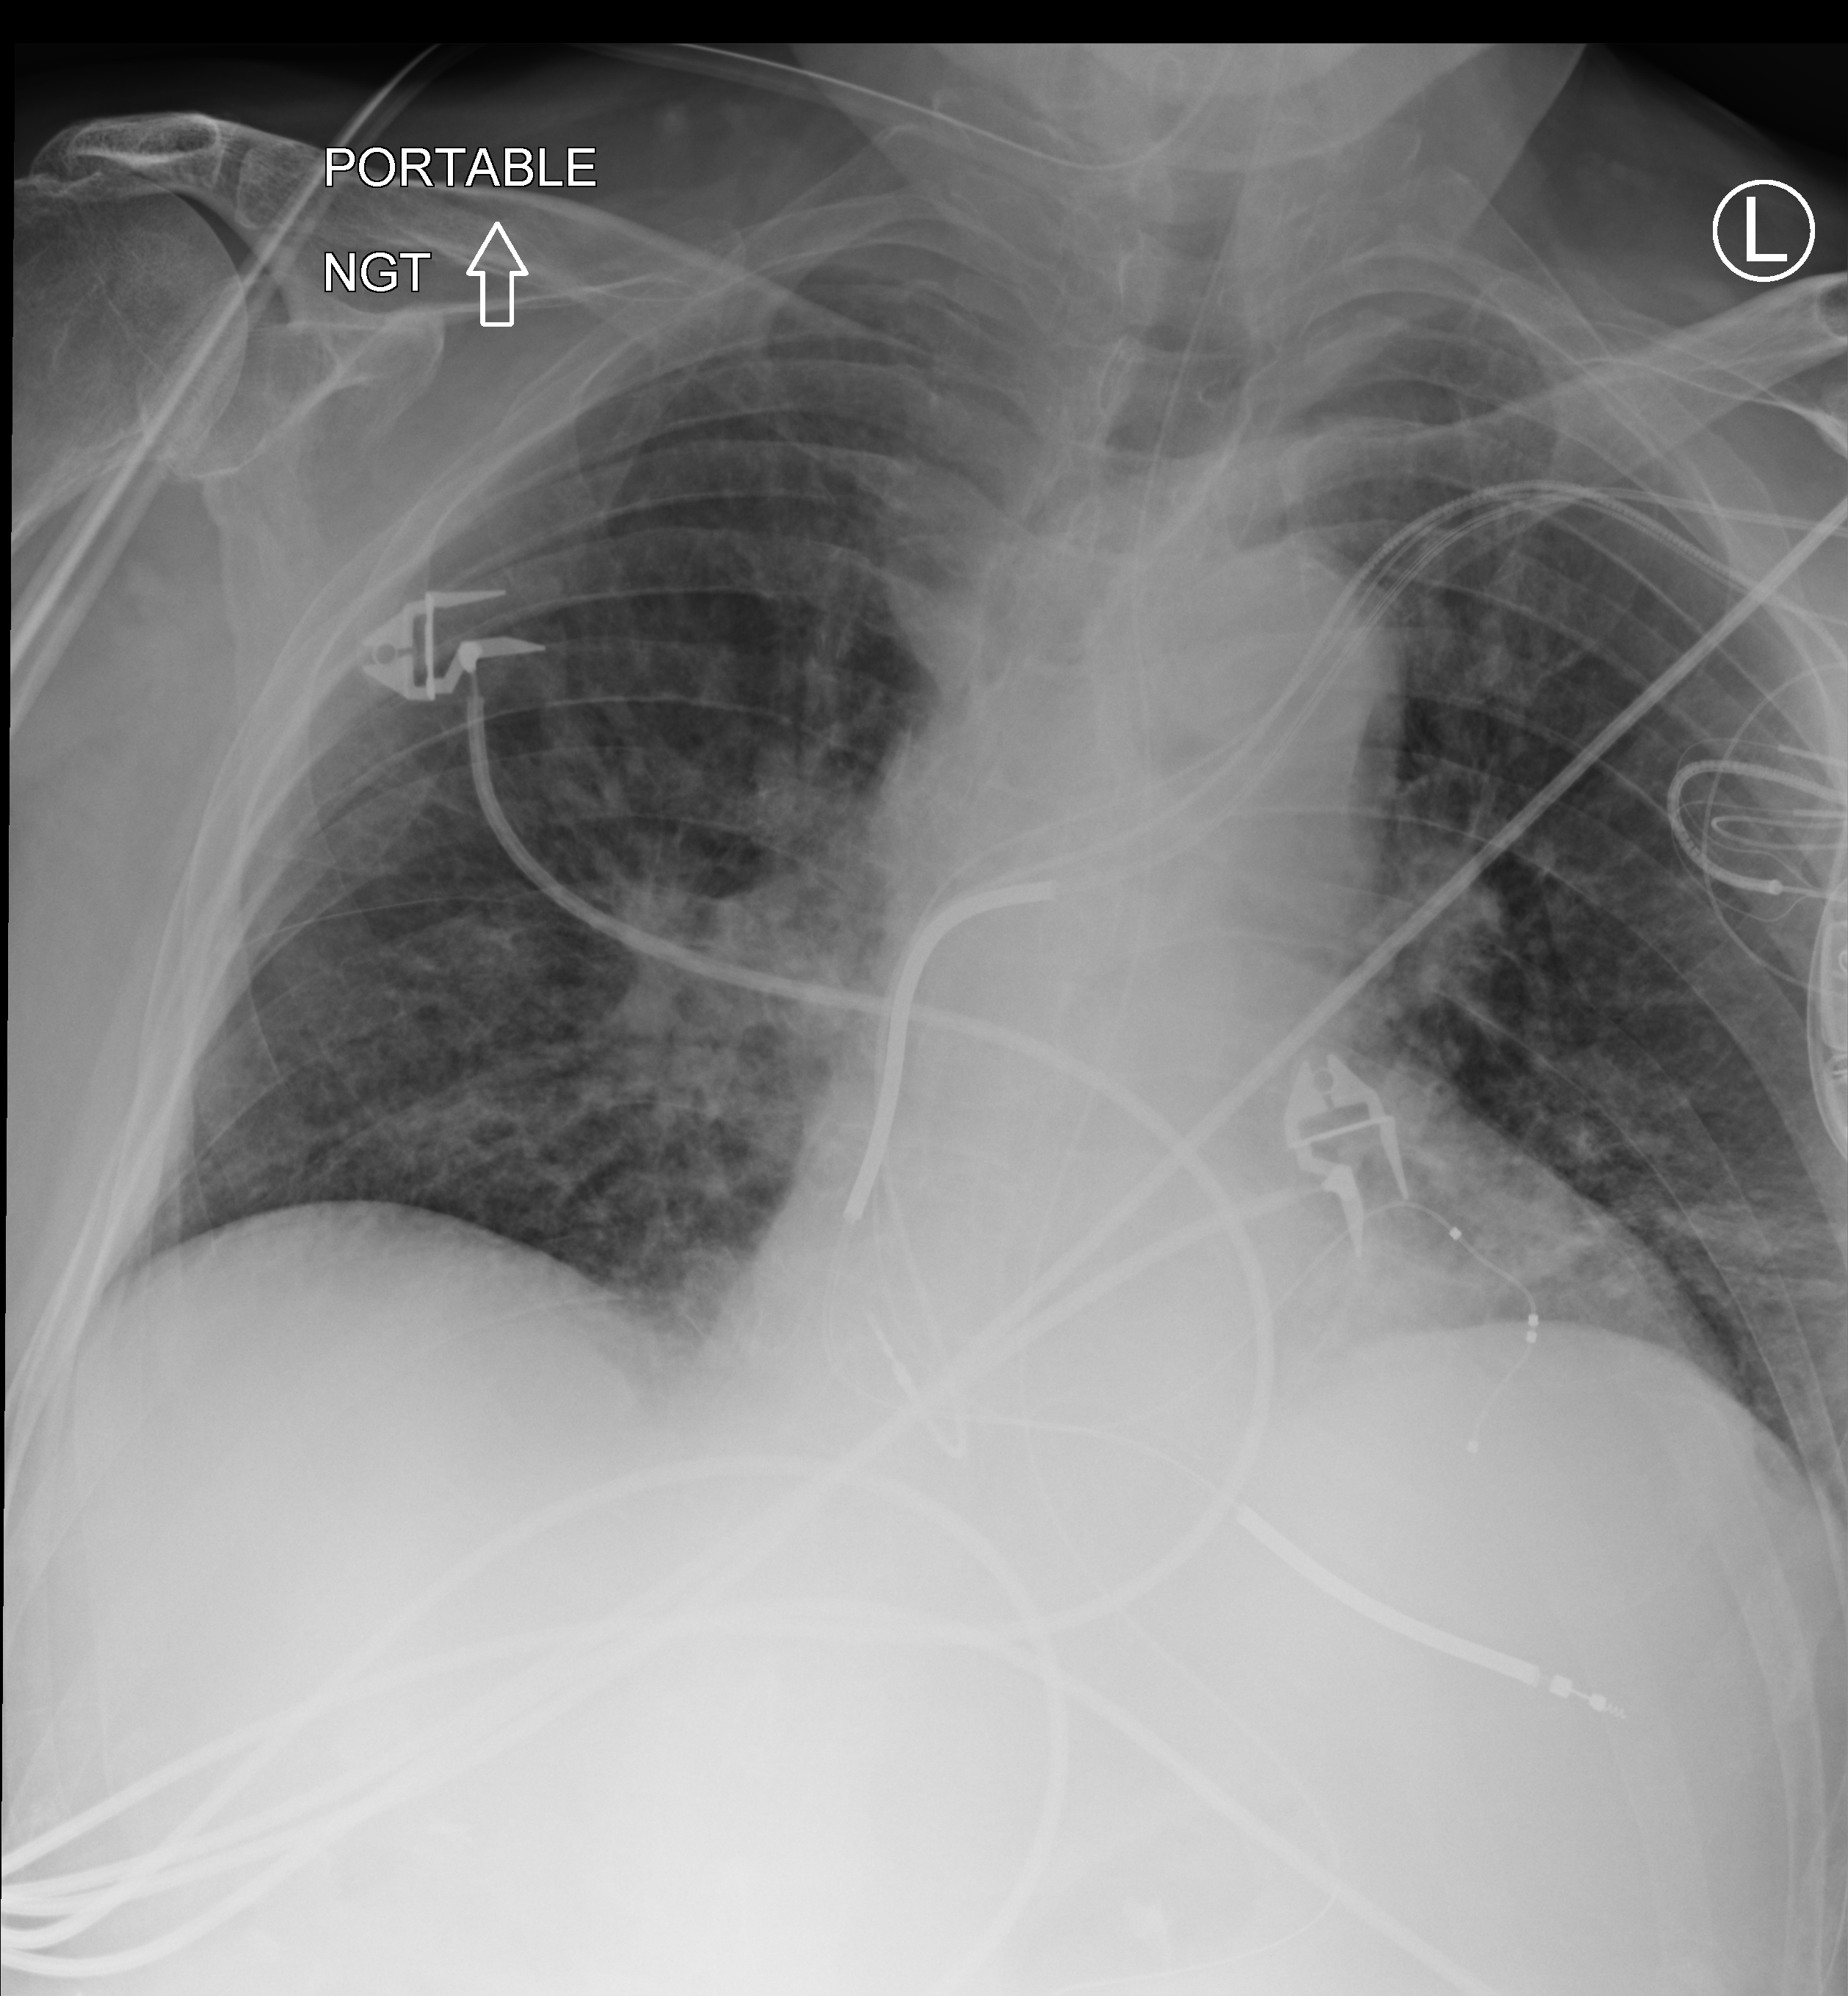
Chest X-ray (portable); anteroposterior (AP) projection. Male patient hospitalised with COVID-19, age 75–90 years.
Hospital-stay facts (about this admission, not read from this image; timing relative to this image not recorded): length of hospital stay: 4 days; admitted to intensive care during this hospital stay: no; mechanically ventilated during this hospital stay: no.